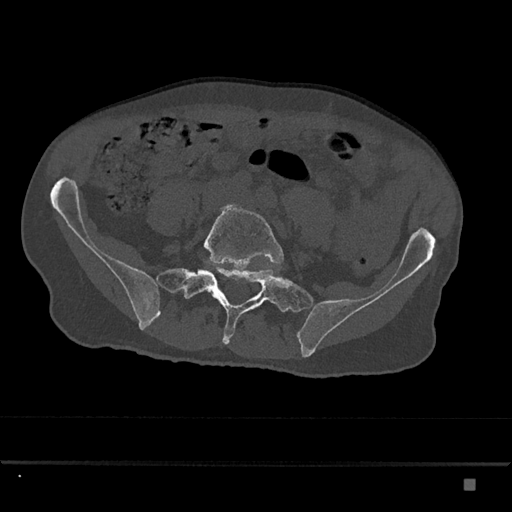
CT including the spine, one axial slice; position 250 of 797 along the scan axis; reconstruction kernel Br40s/3; bone window (W 1800 / L 400 HU); 0.5 mm slice thickness; 512 × 512 image matrix, field of view 390 × 390 mm. Male patient, age 72 years. From the clinical record (not read from this slice): primary cancer: prostate.
Annotated regions visible in this slice (semi-automatically segmented with operator editing):
- L5 vertebra: bounding box <203,204,283,292> (left, top, right, bottom; pixels)